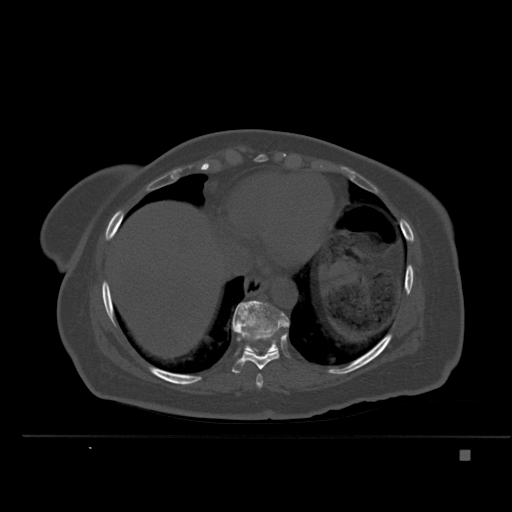
CT including the spine, one axial slice; position 294 of 477 along the scan axis; bone window (W 1800 / L 400 HU); 512 × 512 image matrix, field of view 422 × 422 mm. Patient: female, 74 years. From the clinical record (not read from this slice): primary cancer: colon.
Structures marked on this image (semi-automatically segmented with operator editing):
- T10 vertebra: bounding box [x1, y1, x2, y2] px = [234, 300, 287, 352]
- T8 vertebra: [256, 374, 263, 388]
- T9 vertebra: [232, 306, 289, 373]